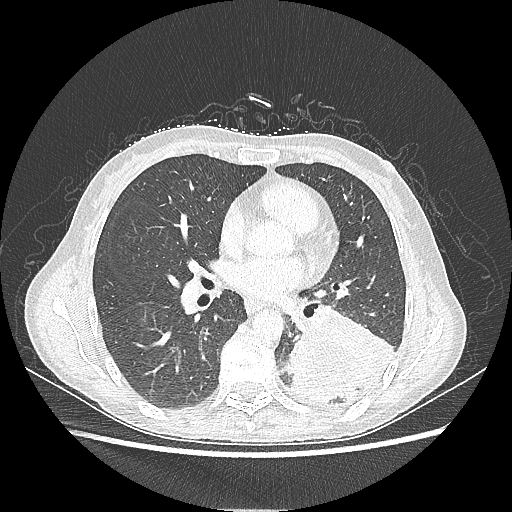
Chest CT, one axial slice; reconstruction kernel LUNG; 80 kVp; lung window (W 1500 / L -600 HU); 512 × 512 image matrix. Patient: female, 53 years. From the clinical record (not read from this slice): clinical TNM (as recorded): T3 N0 M0.
Structures marked on this image (bounding box drawn by a radiologist):
- lung tumour (recorded histology: adenocarcinoma): box from (x=287, y=310) to (x=396, y=408) px